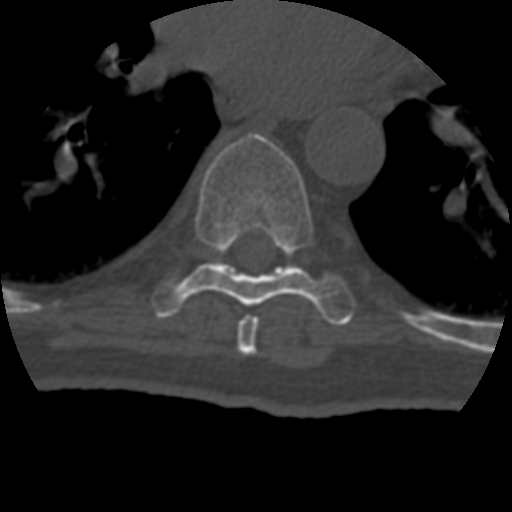
CT including the spine, one axial slice; position 260 of 399 along the scan axis; reconstruction kernel STANDARD; 120 kVp; bone window (W 1800 / L 400 HU); 1.25 mm slice thickness; 512 × 512 image matrix, field of view 160 × 160 mm. Patient age 69 years. From the clinical record (not read from this slice): primary cancer: prostate.
Structures marked on this image (semi-automatically segmented with operator editing):
- T7 vertebra: bounding box [x1, y1, x2, y2] px = [237, 315, 259, 356]
- T8 vertebra: [152, 133, 355, 326]